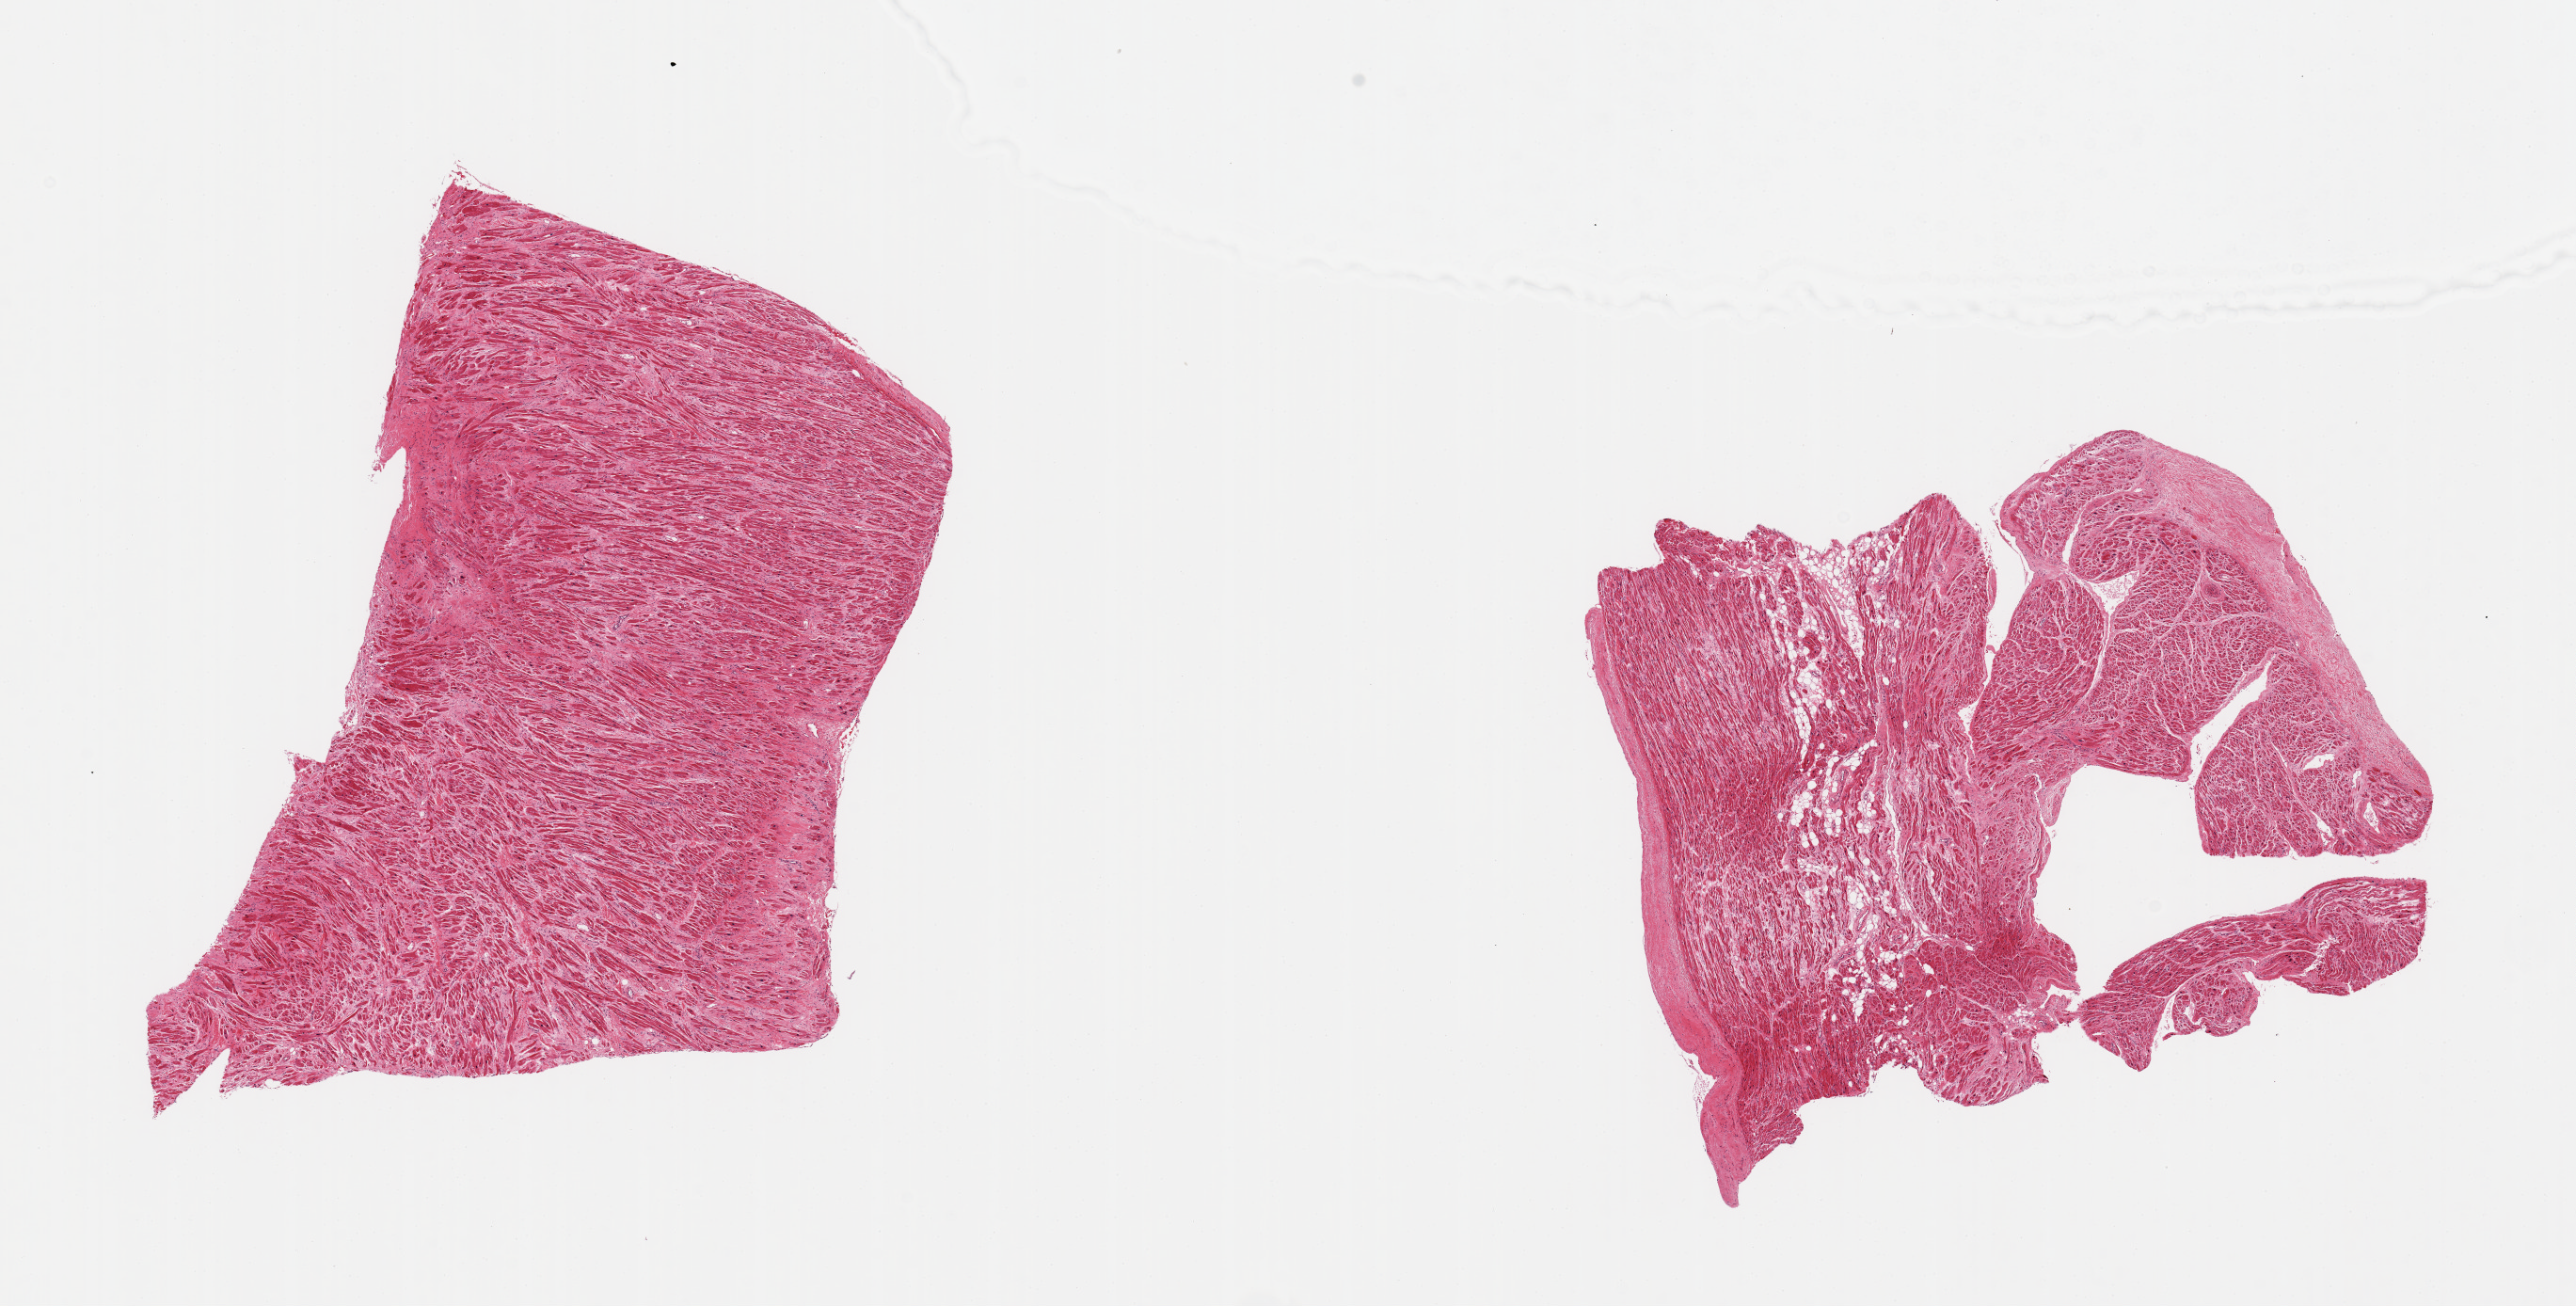
Digitized haematoxylin and eosin-stained section, brightfield, low-resolution overview of the scanned area, about 21.7 x 11.0 mm, PAXgene-fixed paraffin-embedded (PFPE) section, target tissue: auricular appendage, tissue donor sample. Donor: male.
Reviewer comment on this tissue sample: 2 pieces, no abnormalities.